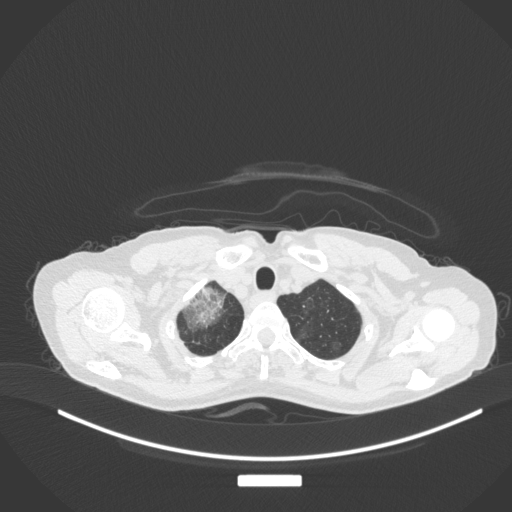
Chest CT, one axial slice; slice 297 of 311 in the series (ordered by position); reconstruction kernel B31f; lung window (W 1500 / L -600 HU); 1 mm slice thickness; 512 × 512 image matrix, field of view 400 × 400 mm. Patient: female, 59 years. From the clinical record (not read from this slice): clinical TNM (as recorded): T3 N0 M0.
Annotated regions visible in this slice (bounding box drawn by a radiologist):
- lung tumour (recorded histology: adenocarcinoma): bounding box <177,285,228,327> (left, top, right, bottom; pixels)